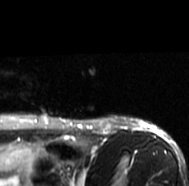
MRI of an extremity soft-tissue mass, one axial slice; position 63 of 77 along the scan axis; T2-weighted fat-saturated; MR volume resampled by the dataset authors to the PET/CT grid (not the native acquisition matrix); 189 × 186 image matrix, field of view 185 × 182 mm. Female patient. Case-level facts recorded for this patient, not image findings: histological type: leiomyosarcoma; grade: high; site of the primary tumour: groin.
Structures marked on this image (expert contour drawn on MRI and transferred to this co-registered scan by the dataset authors):
- gross tumour volume including surrounding oedema: box from (x=97, y=116) to (x=141, y=128) px